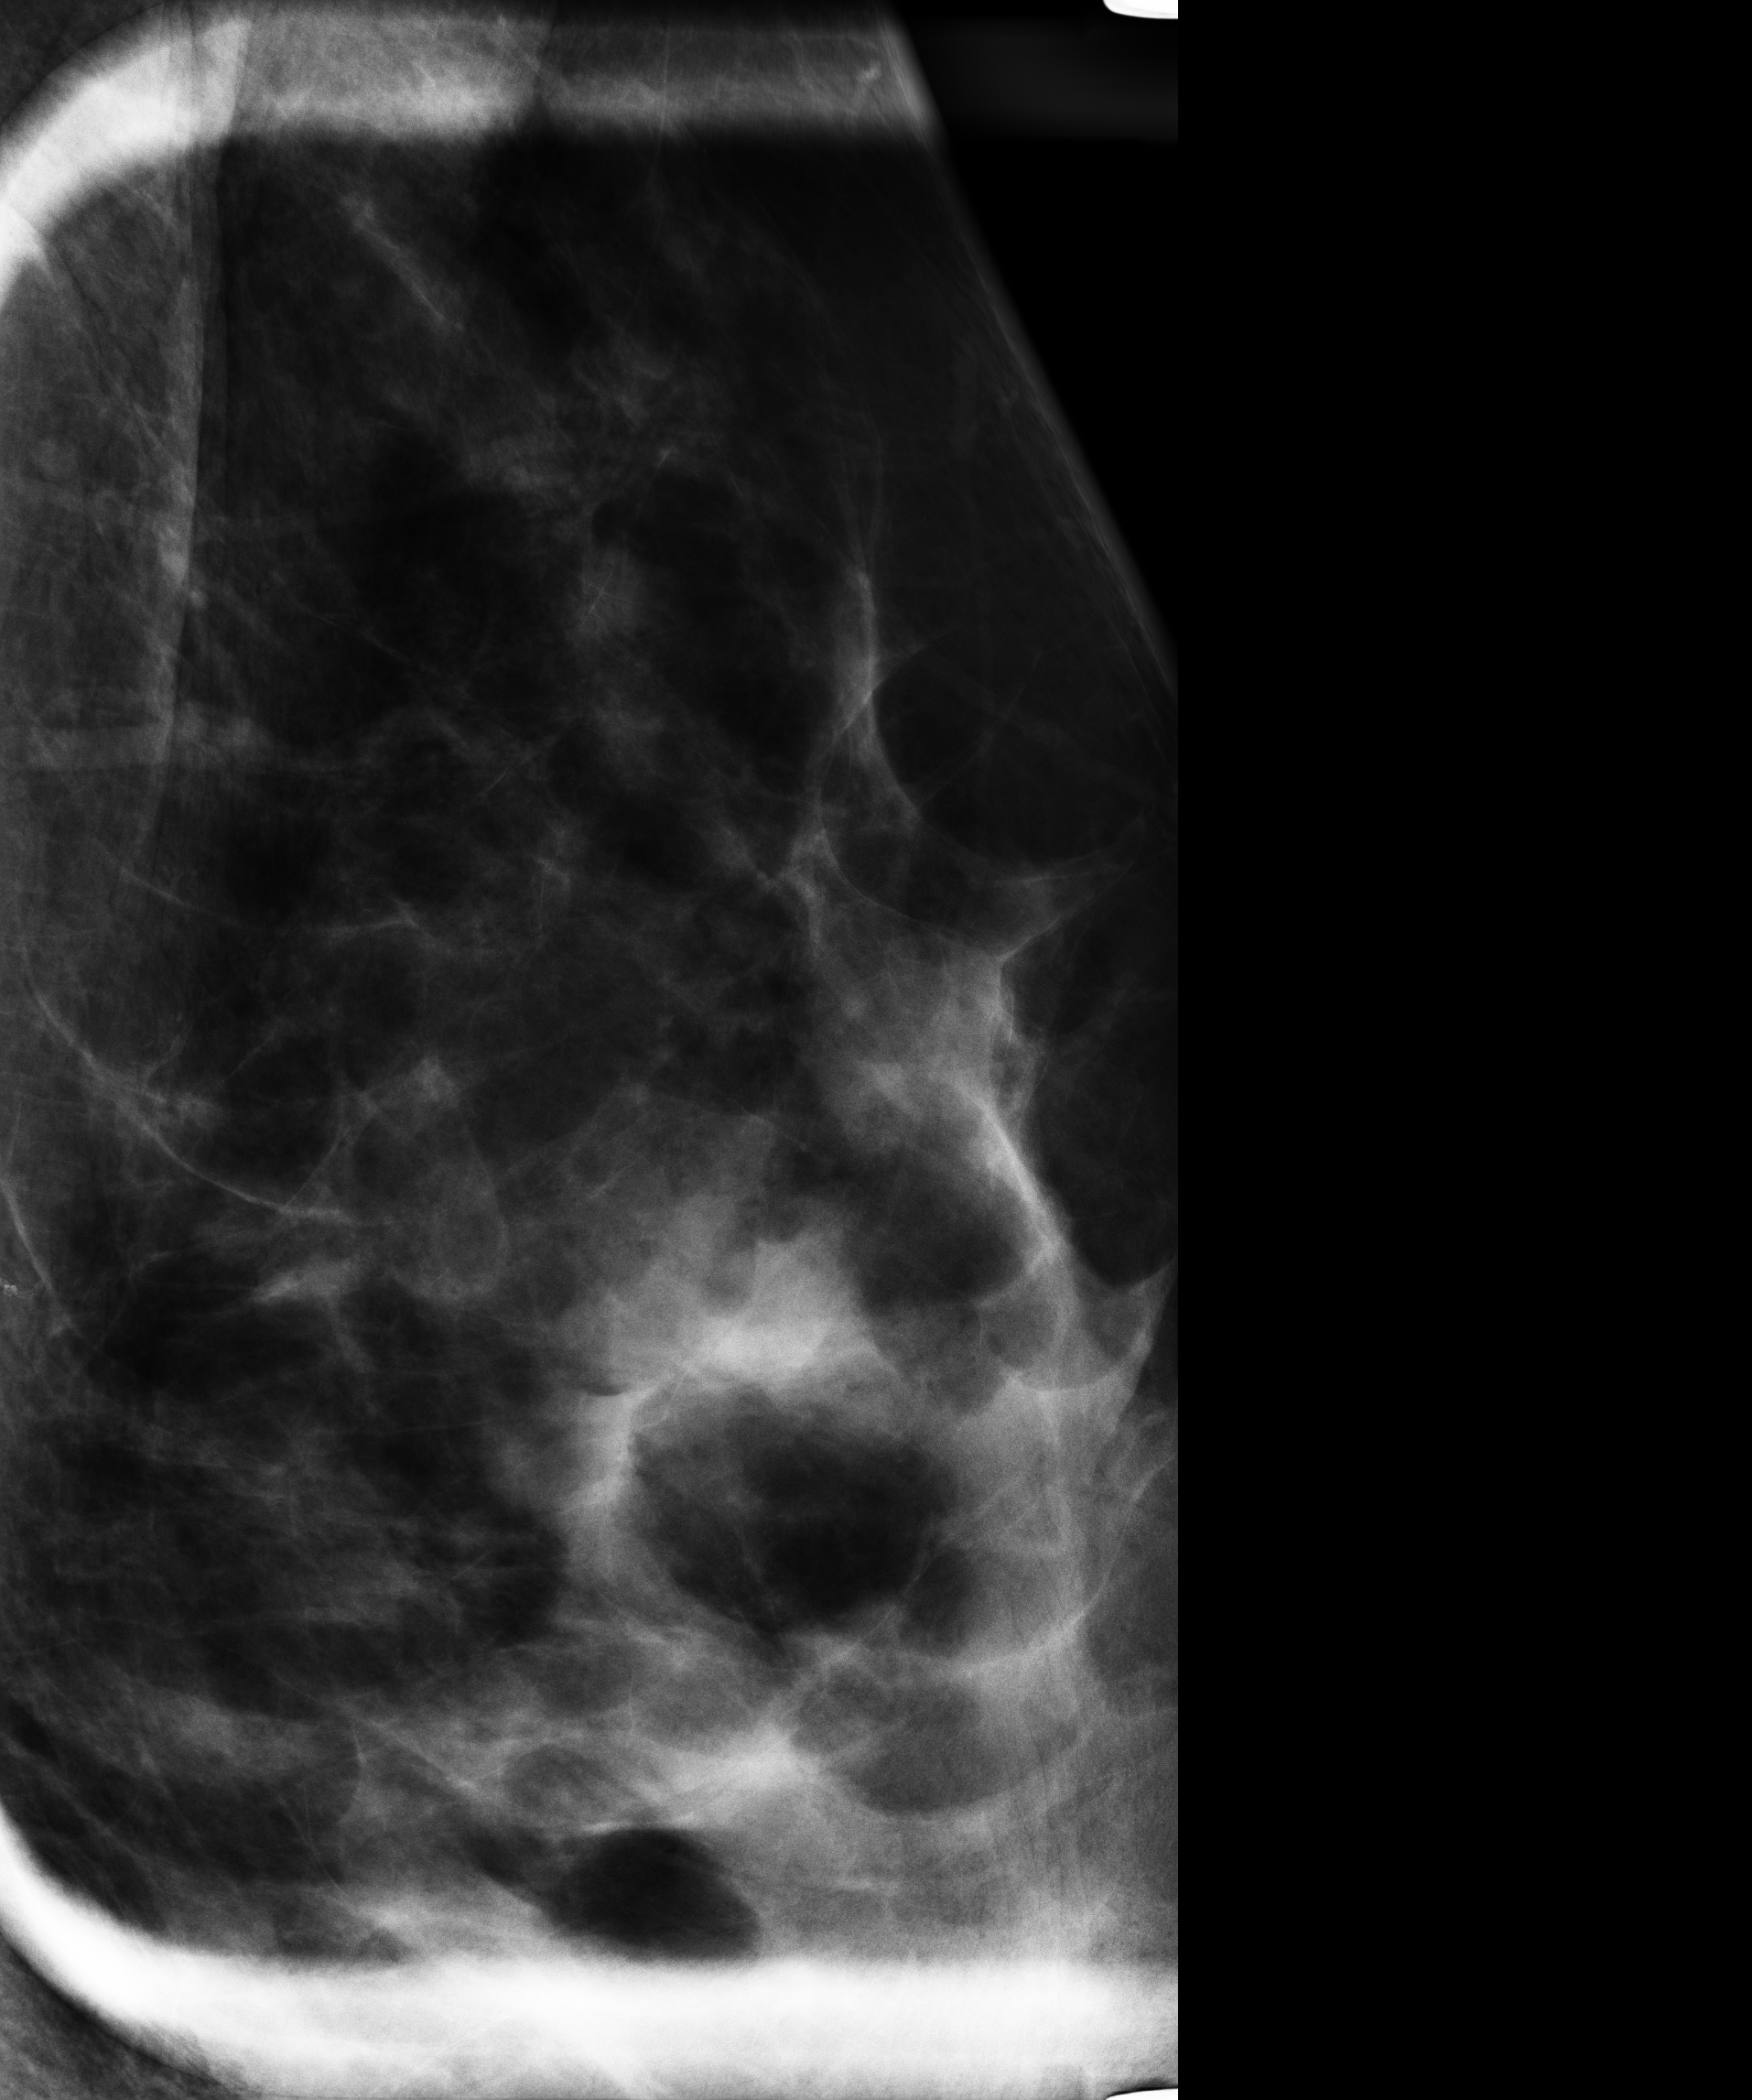
Full-field digital mammogram (FFDM), left breast, mediolateral (ML) view, diagnostic examination (additional views), compressed breast thickness 48 mm, system: Senographe Essential VERSION ADS_54.11. Patient aged 54 years (female).
- breast density at the screening exam (both breasts): heterogeneously dense (BI-RADS density category c)
- final BI-RADS category for the screening round (tomosynthesis exam, both breasts): category 3
- recall: recalled for additional imaging after this screen